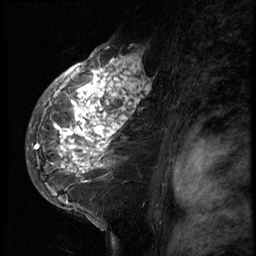
Breast MRI (dynamic contrast-enhanced), one sagittal slice. Slice 46 of 66 in the series (ordered by position). 3 images stored at this slice position (order not interpretable as contrast timing). 1.5 T. TE 4.2 ms, TR 8.9 ms. 256 × 256 image matrix. Female patient, age 39 years. From the clinical record (not read from this slice): setting: breast cancer imaged before/during neoadjuvant chemotherapy; receptor status: HER2-positive.
Outlined on this slice (semi-automatic segmentation, software-assisted and operator-edited):
- analysis volume of interest (the breast-tissue region the enhancement analysis was run in; not a lesion): box from (x=29, y=44) to (x=166, y=196) px
- tumour enhancement mask (voxels above the 140 % enhancement threshold inside the analysis volume of interest): (x=33, y=46)–(x=152, y=182)